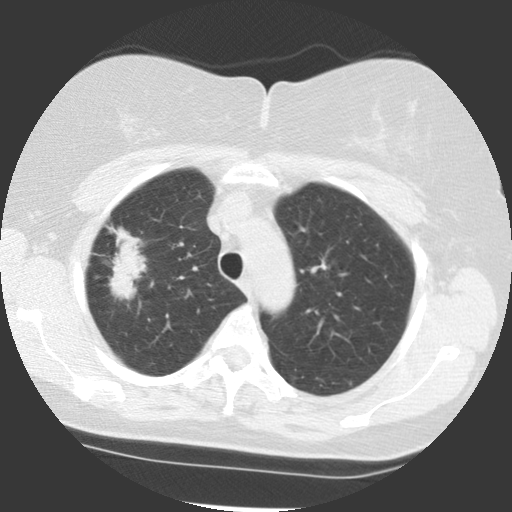
Low-dose screening chest CT, one axial slice; slice 90 of 113 in the series (ordered by position); reconstruction kernel STANDARD; lung window (W 1500 / L -600 HU); 2.5 mm slice thickness; 512 × 512 image matrix, field of view 320 × 320 mm.
Structures marked on this image (manually delineated by an expert):
- lesion 1 (tumor, upper lobe of right lung): bounding box (x1, y1, x2, y2) in pixels: (109, 226, 153, 300)